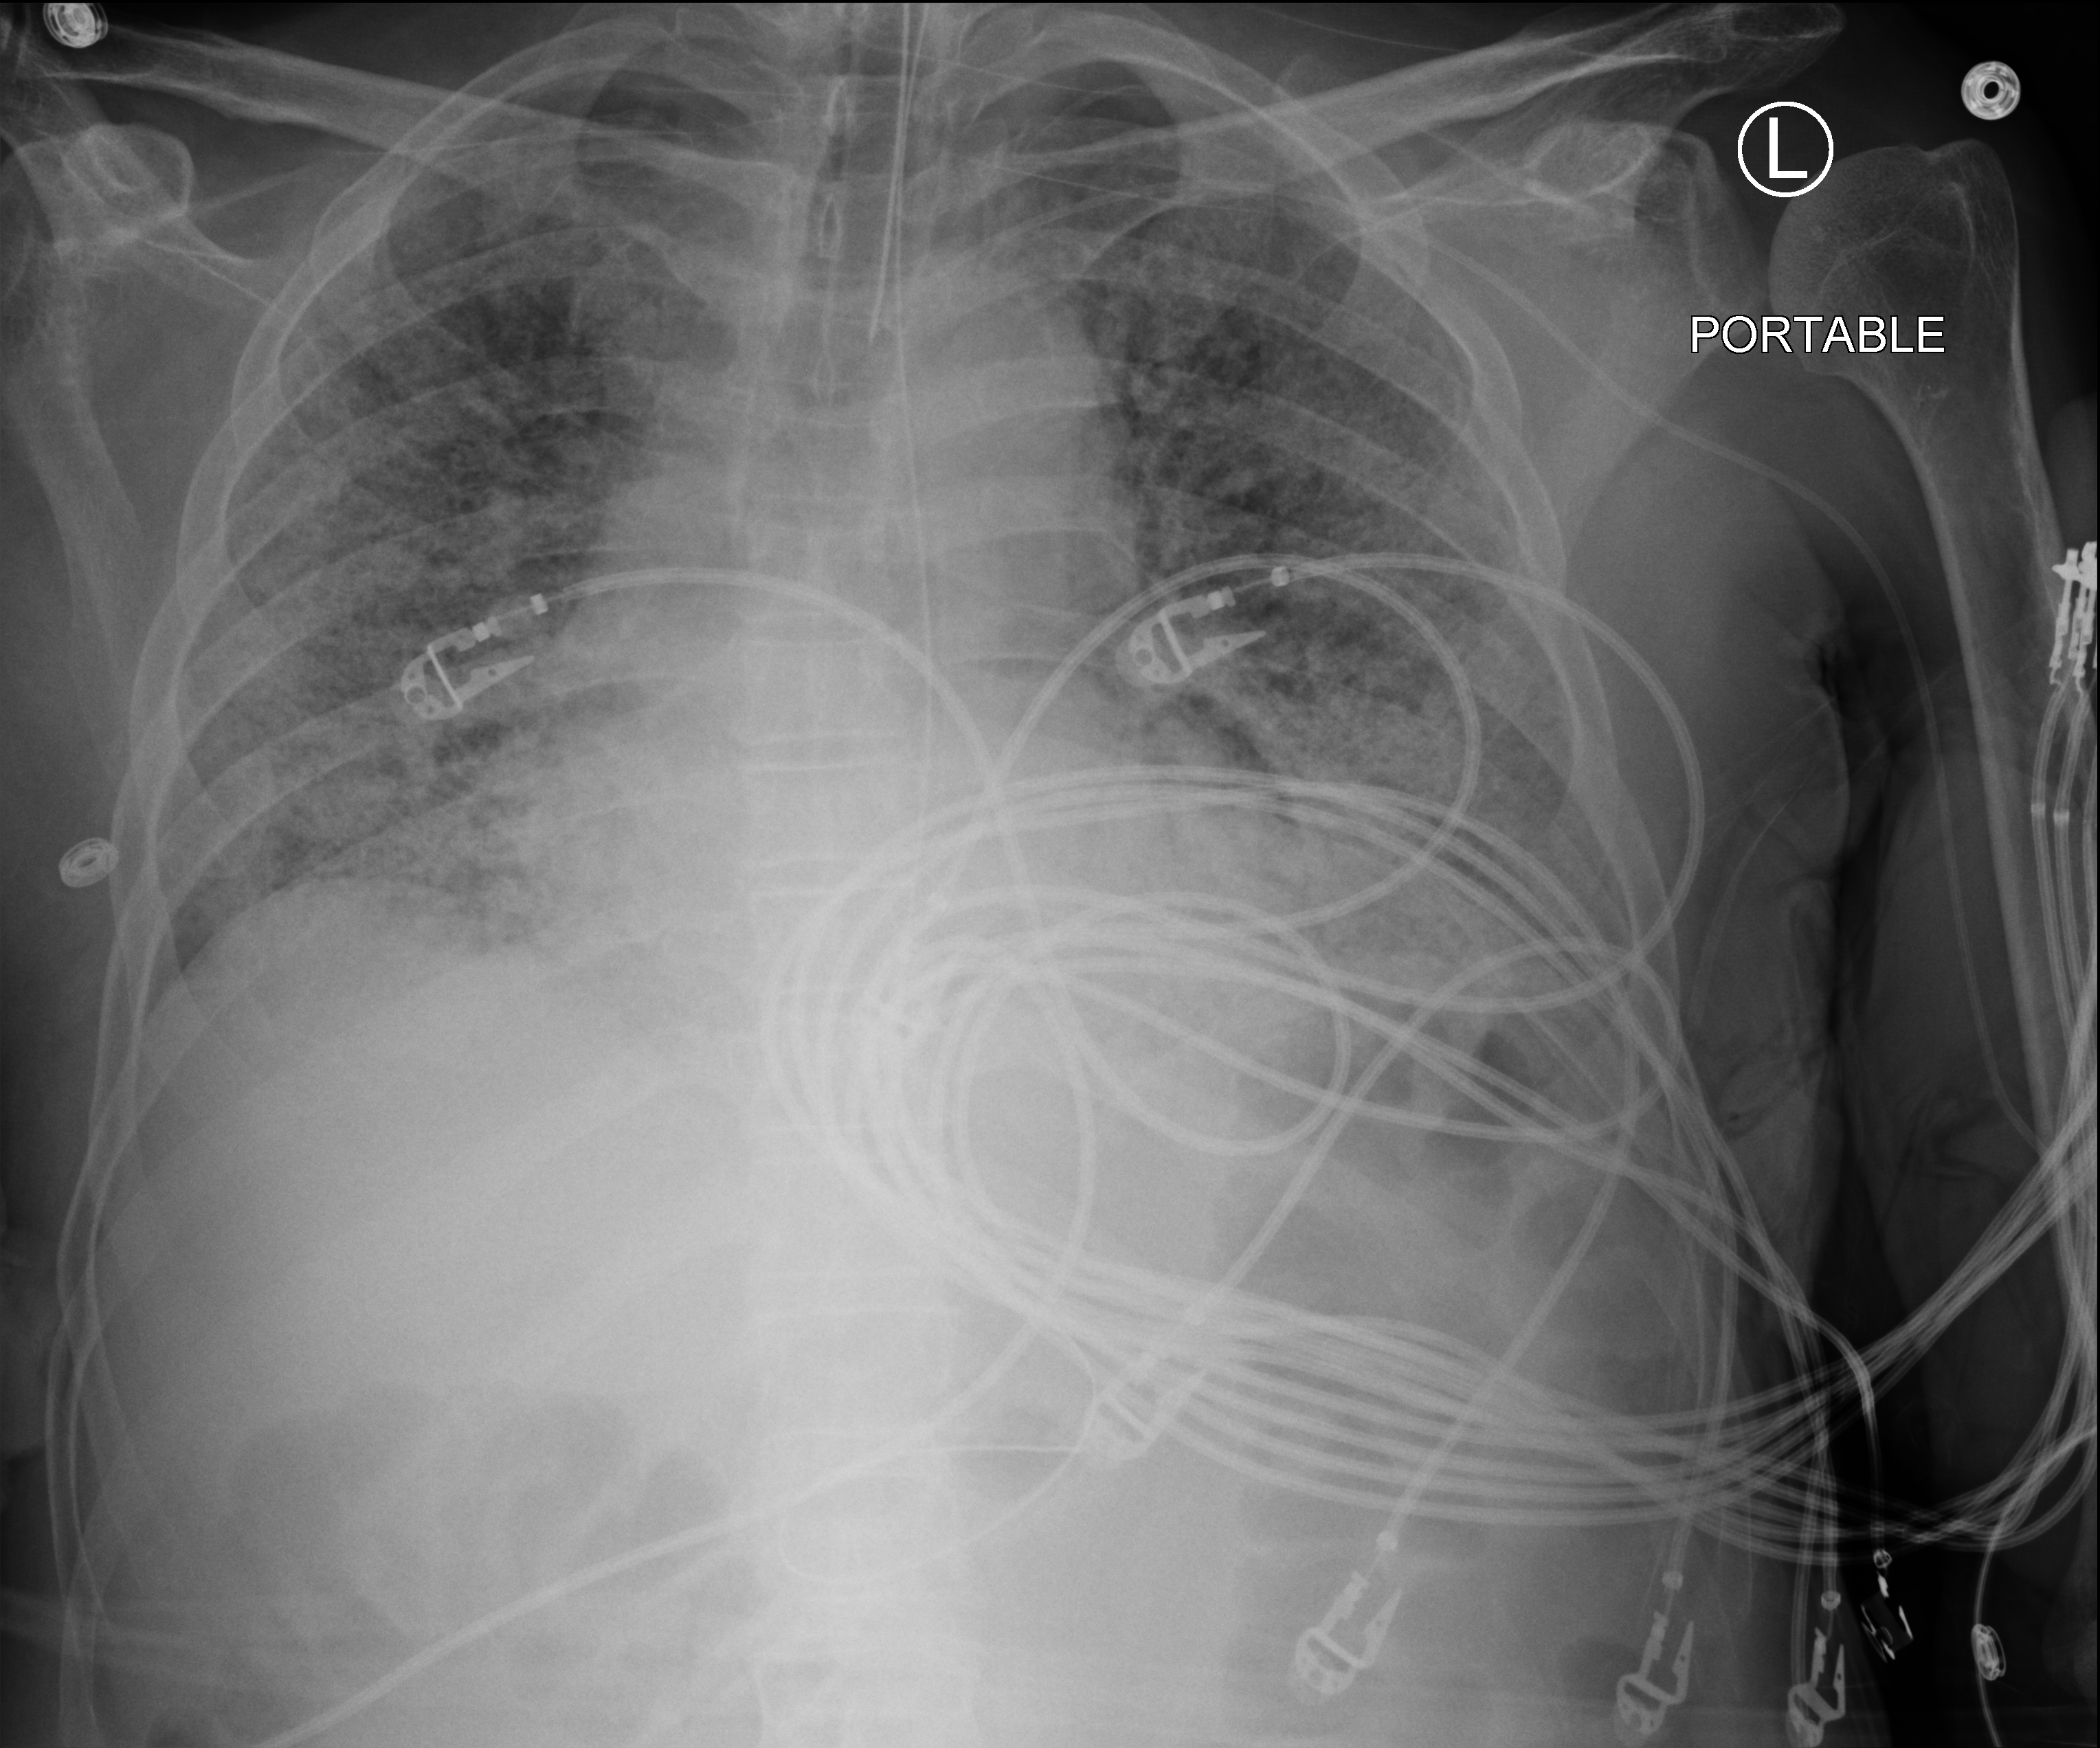
Chest X-ray (portable). Patient hospitalised with COVID-19; male, aged 60–74 years.
Hospital-stay facts (about this admission, not read from this image; timing relative to this image not recorded):
- admitted to intensive care during this hospital stay: yes
- length of hospital stay: 54 days